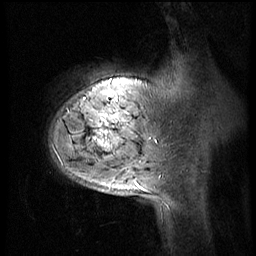
Breast MRI (dynamic contrast-enhanced), one sagittal slice; slice 9 of 56 in the series (ordered by position); 4 images stored at this slice position (order not interpretable as contrast timing); 1.5 T; TE 4.2 ms, TR 8.9 ms; 2.5 mm slice thickness; 256 × 256 image matrix. Female patient, age 51 years. Case-level facts recorded for this patient, not image findings: setting: breast cancer imaged before/during neoadjuvant chemotherapy; receptor status: triple-negative.
Annotated regions visible in this slice (semi-automatic segmentation, software-assisted and operator-edited):
- analysis volume of interest (the breast-tissue region the enhancement analysis was run in; not a lesion): bounding box <48,70,150,173> (left, top, right, bottom; pixels)
- tumour enhancement mask (voxels above the 140 % enhancement threshold inside the analysis volume of interest): <99,128,112,149>